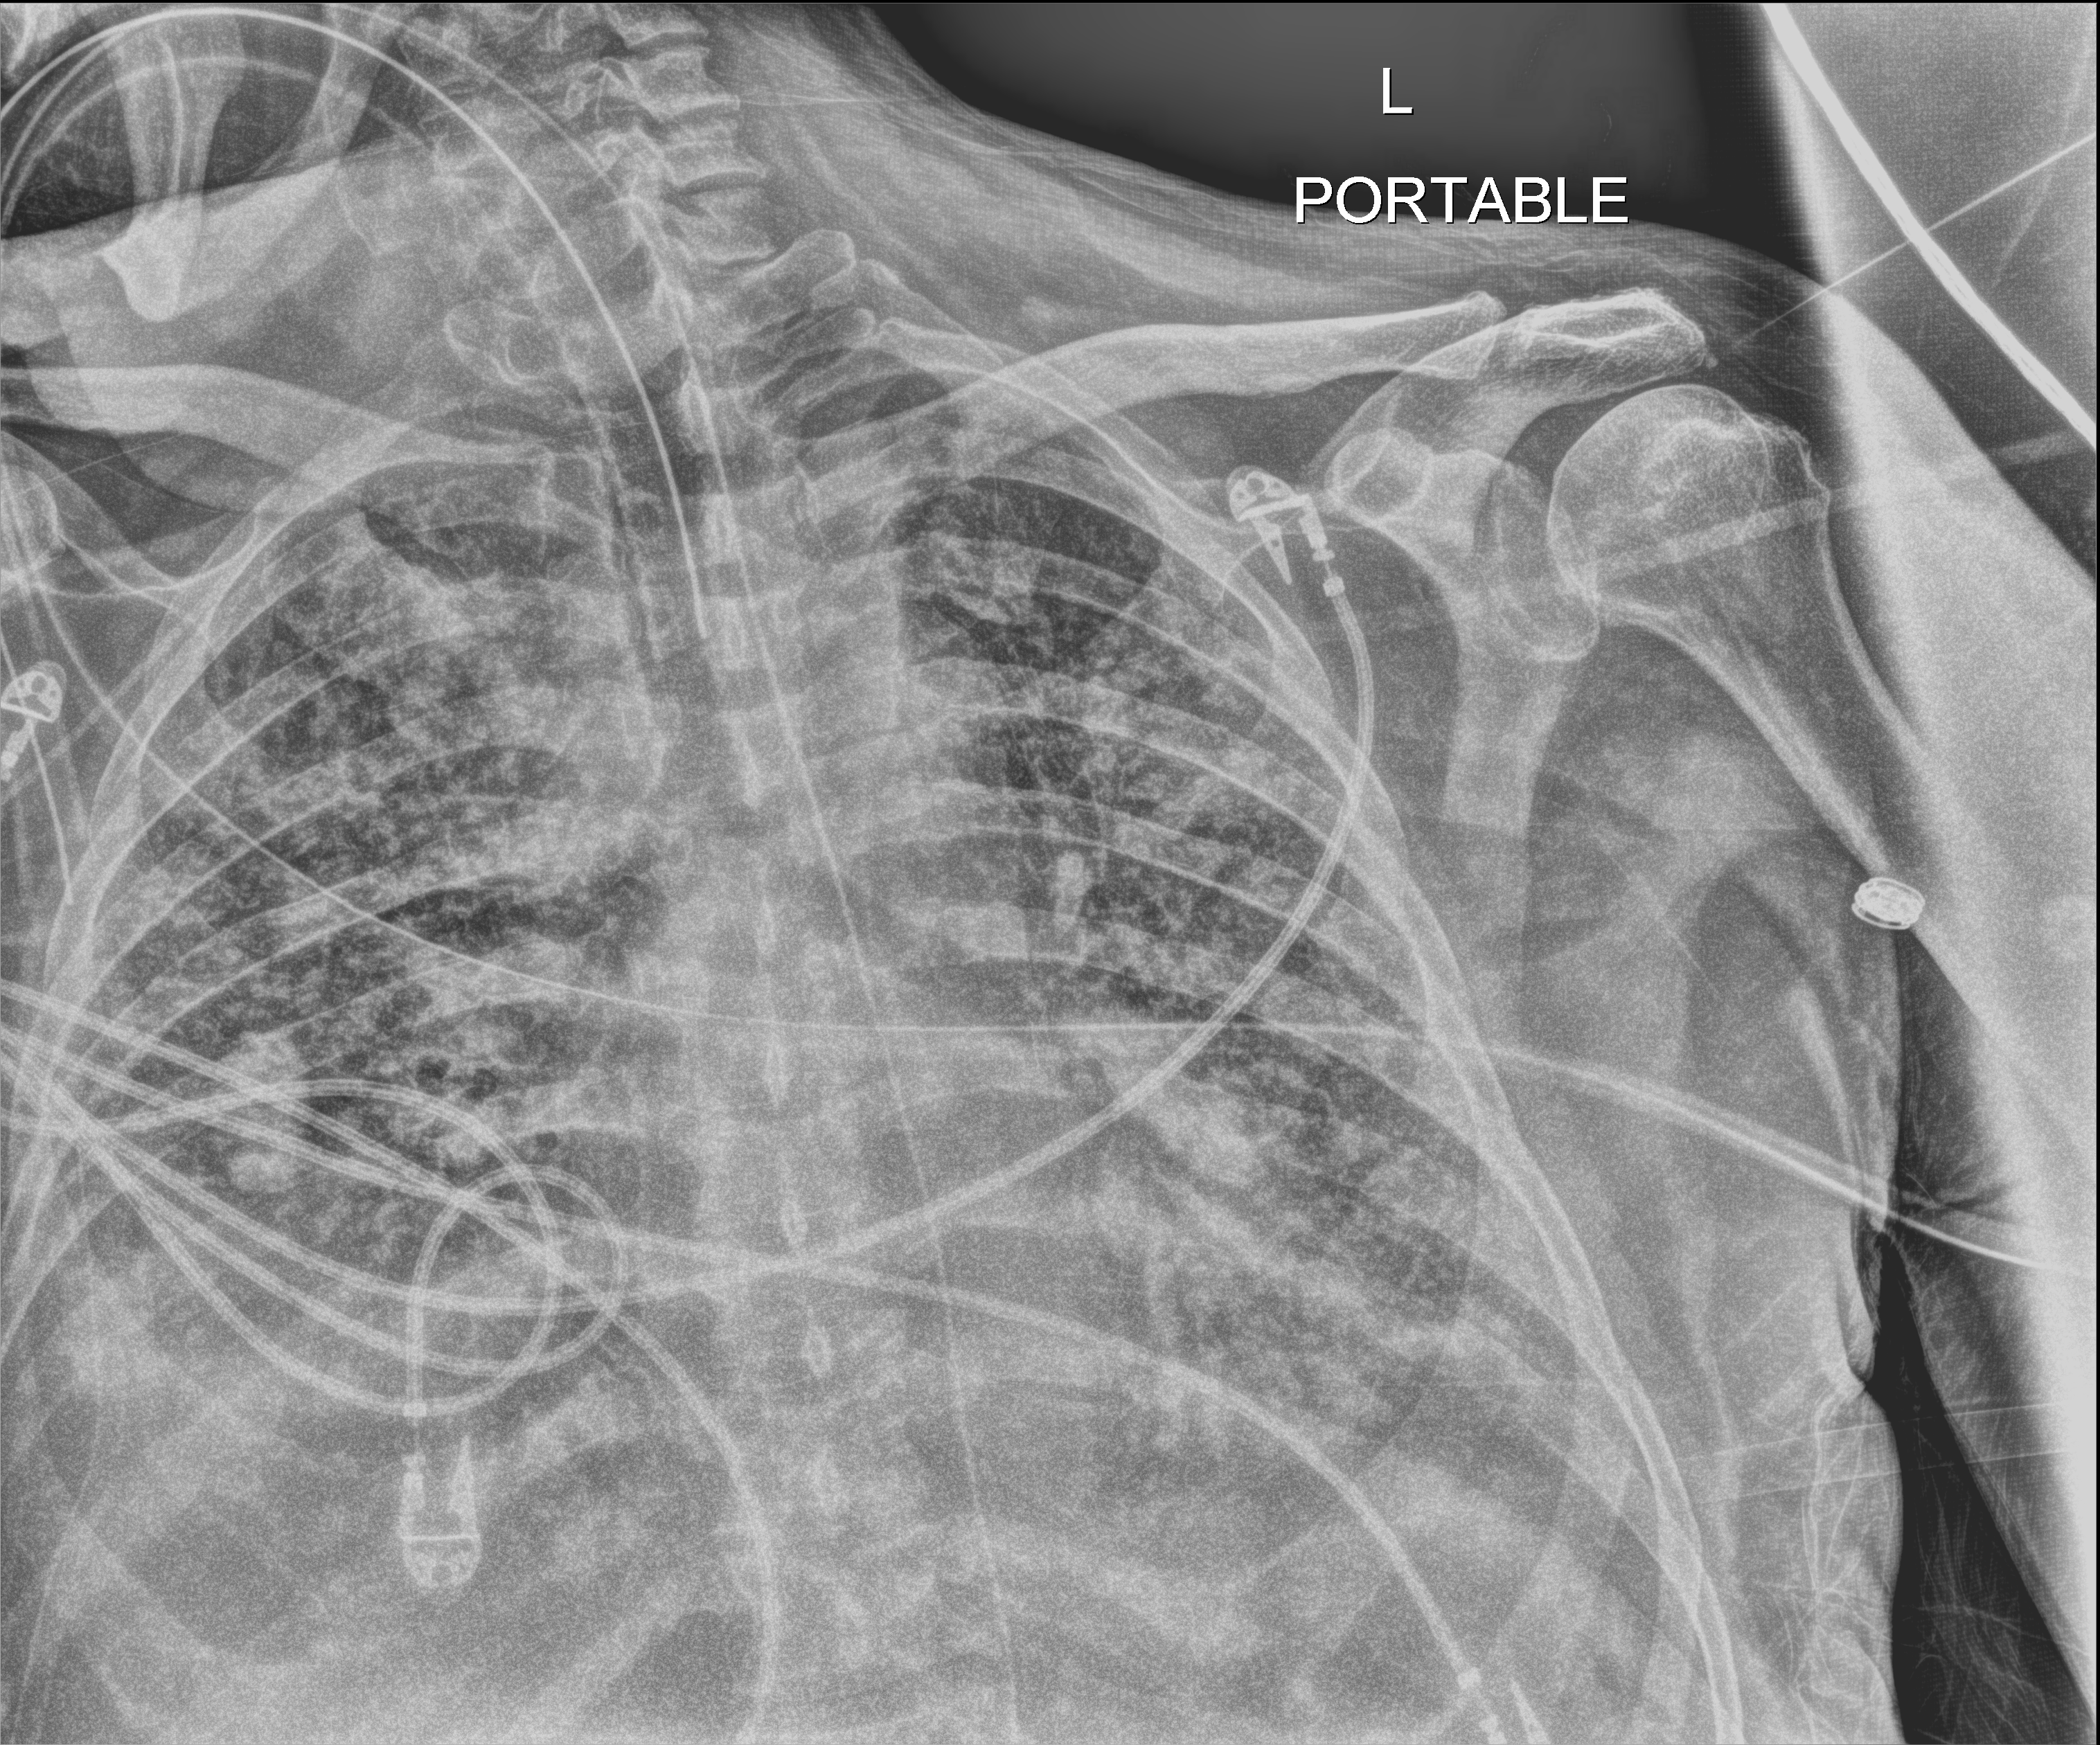
Bedside chest radiograph (digital radiography), anteroposterior (AP) projection. Male patient hospitalised with COVID-19, age 60–74 years.
Admission-level facts for this patient (not findings on this image; timing relative to this image not recorded):
- COPD (admission record): no